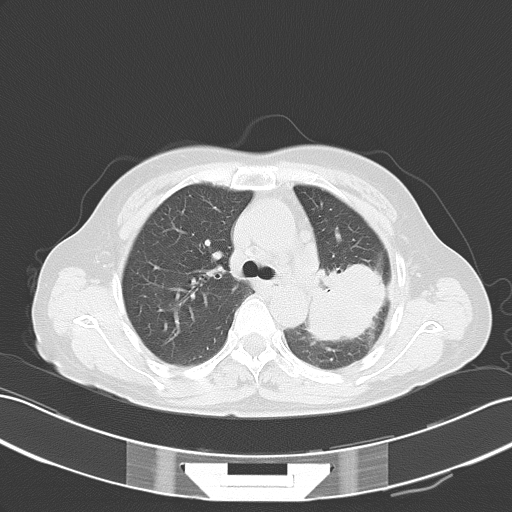
Chest CT, one axial slice. Slice 34 of 51 in the series (ordered by position). Reconstruction kernel B70f. Lung window (W 1500 / L -600 HU). 512 × 512 image matrix, field of view 353 × 353 mm. Patient: female, 54 years. From the clinical record (not read from this slice): clinical TNM (as recorded): T3 N1 M0.
Structures marked on this image (bounding box drawn by a radiologist):
- lung tumour (recorded histology: adenocarcinoma): bounding box (x1, y1, x2, y2) in pixels: (310, 258, 389, 342)